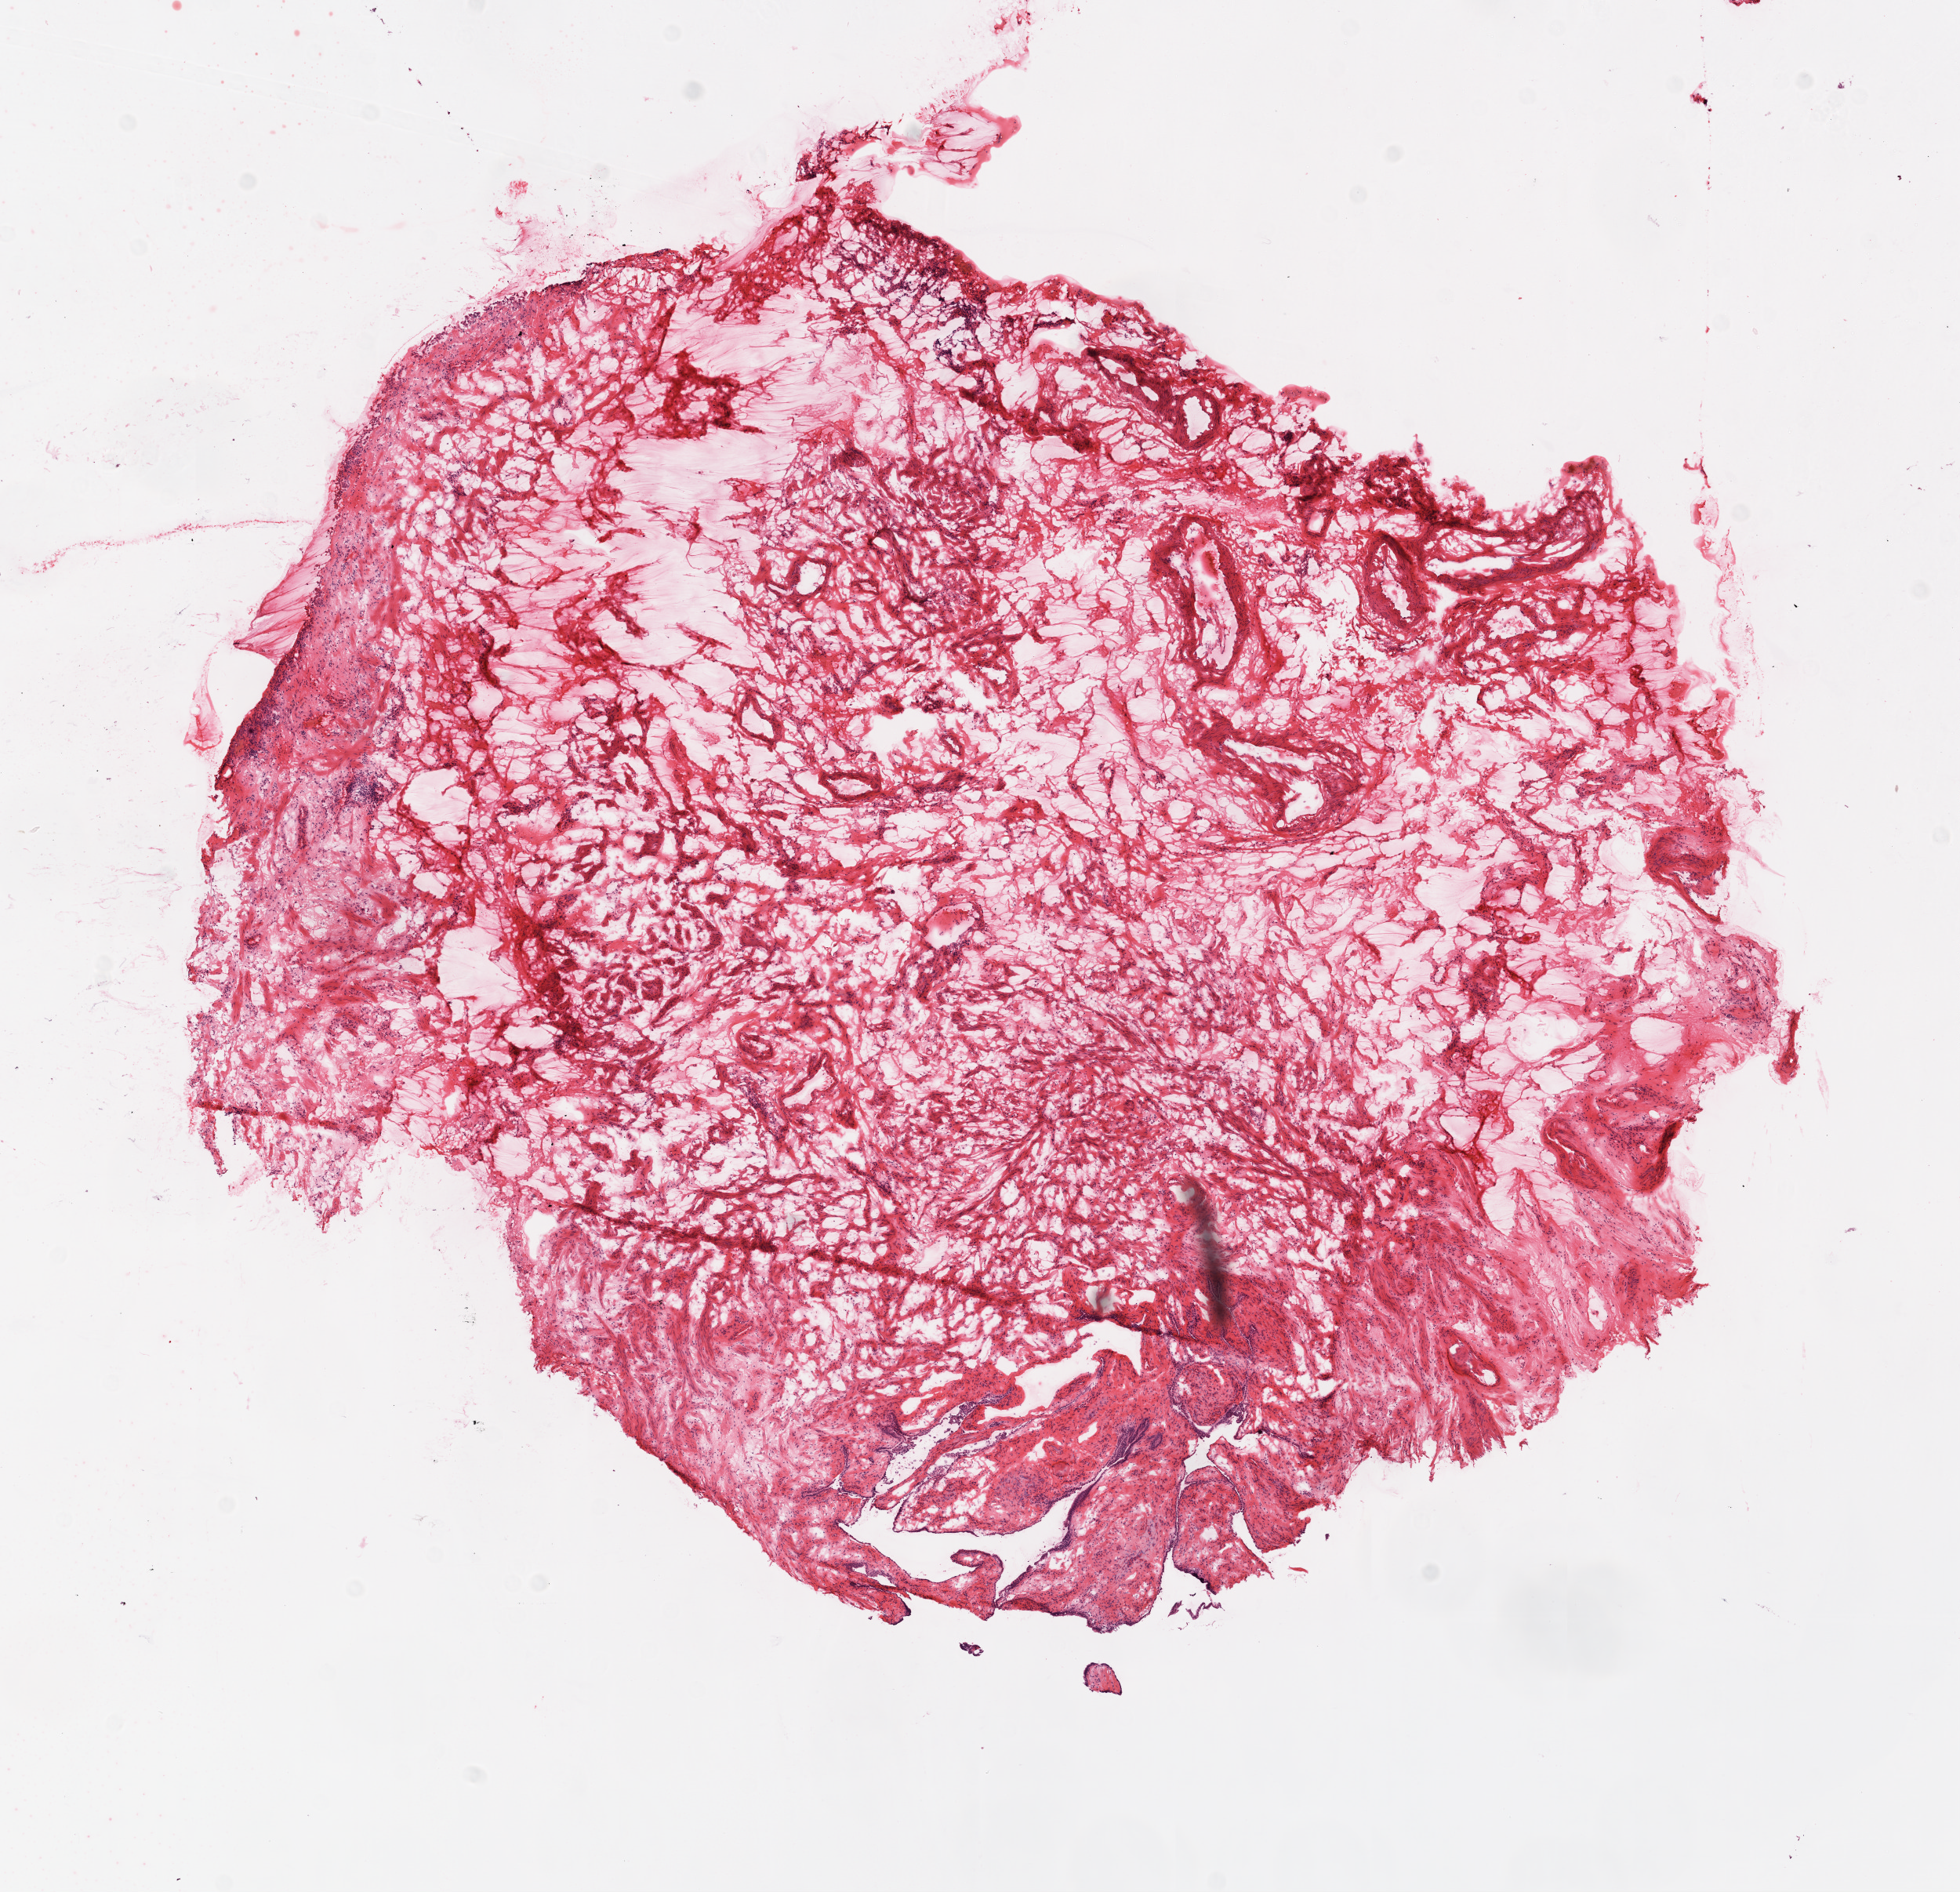
Whole-slide histology image, H&E-stained — a low-resolution overview of the entire scanned area, about 10.0 x 9.7 mm (from a 20x scan), frozen section, sample: solid tissue normal (non-tumour tissue), ovary. Female patient; age at initial diagnosis 65 years.
This section: solid tissue normal sample (biorepository sample class). Patient diagnosis: Serous cystadenocarcinoma, NOS.